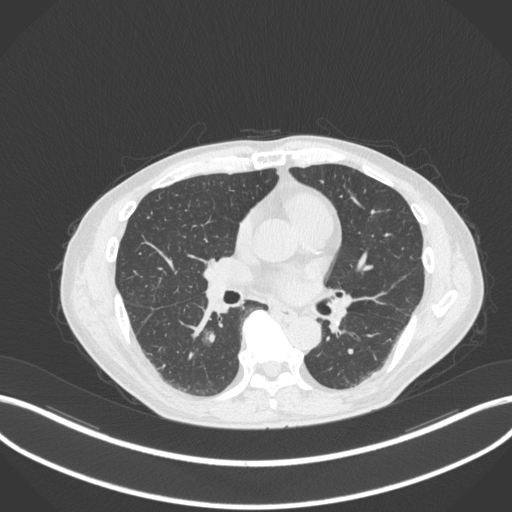
Chest CT, one axial slice. Position 162 of 324 along the scan axis. Reconstruction kernel B31f. 120 kVp. Lung window (W 1500 / L -600 HU). 1 mm slice thickness. 512 × 512 image matrix. Male patient, age 61 years. From the clinical record (not read from this slice): clinical TNM (as recorded): T1c N0 M0.
Structures marked on this image (bounding box drawn by a radiologist):
- lung tumour (recorded histology: adenocarcinoma): box from (x=198, y=325) to (x=218, y=348) px